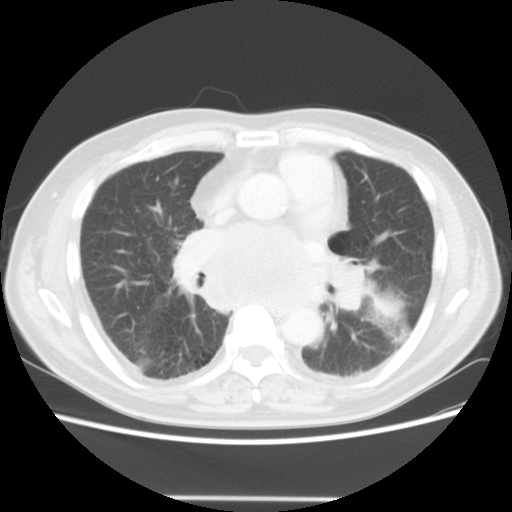
Chest CT, one axial slice; position 26 of 56 along the scan axis; lung window (W 1500 / L -600 HU); 5 mm slice thickness; 512 × 512 image matrix, field of view 360 × 360 mm. Patient: male, 66 years. Case-level facts recorded for this patient, not image findings: clinical TNM (as recorded): T4 N3 M0; histopathological grade: G3.
Annotated regions visible in this slice (rectangle marked by the reading radiologist):
- lung tumour (recorded histology: small cell carcinoma): bounding box [x1, y1, x2, y2] px = [360, 277, 417, 339]